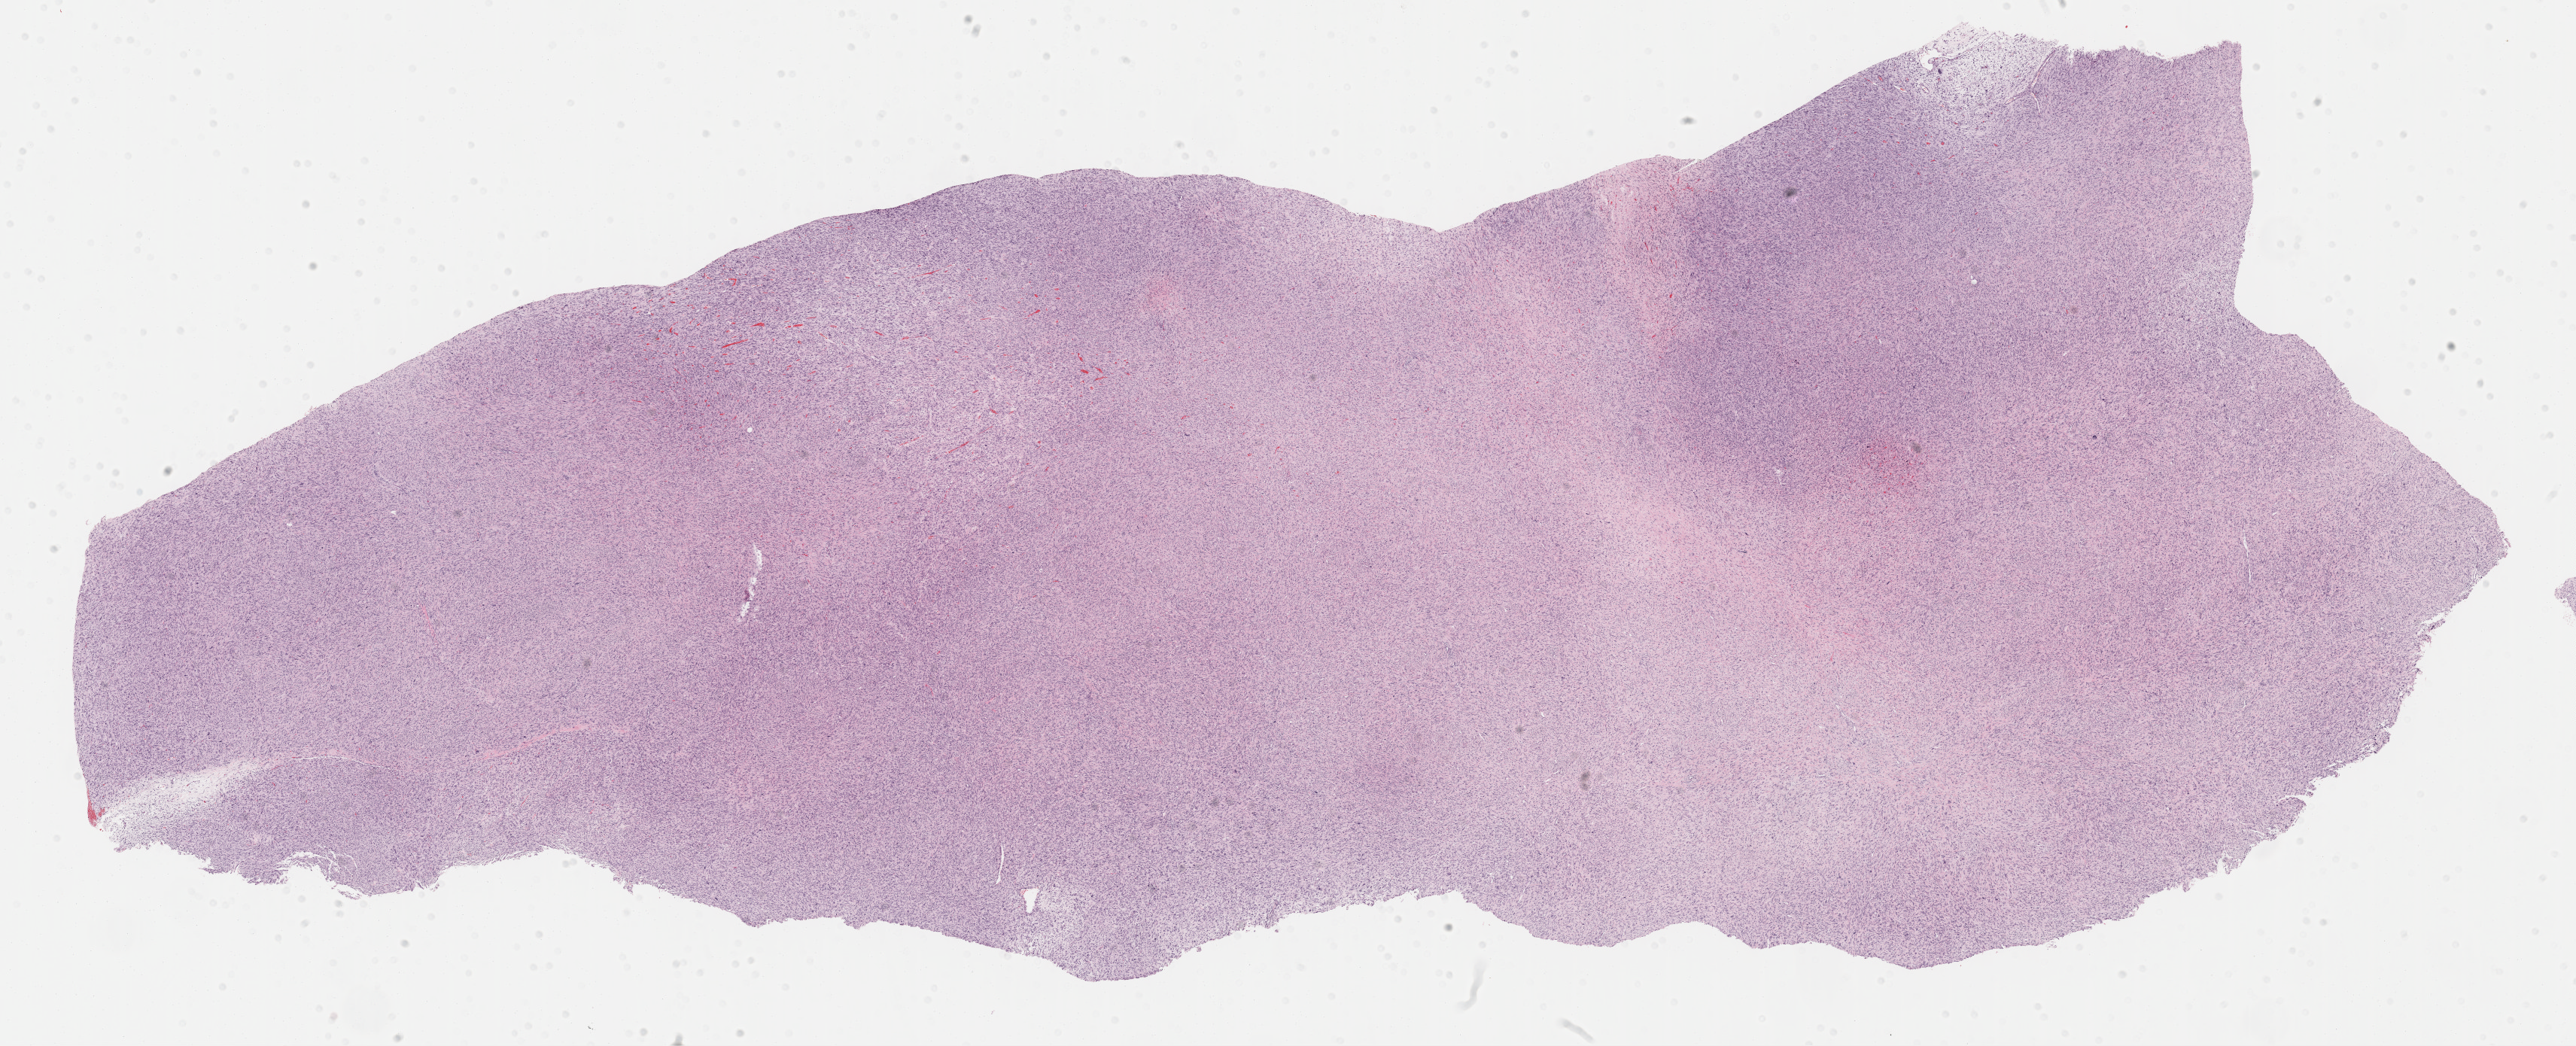
Digitized Hematoxylin and eosin (H&E) stained tissue section (whole slide), shown as a low-resolution overview of the whole scanned area (about 27.7 x 11.2 mm, from a 40x scan), formalin-fixed paraffin-embedded (FFPE) diagnostic section, primary tumour sample from the connective, subcutaneous and other soft tissues. Female, age 63 years at initial diagnosis.
* diagnosis: Malignant fibrous histiocytoma (connective, subcutaneous and other soft tissues of thorax)